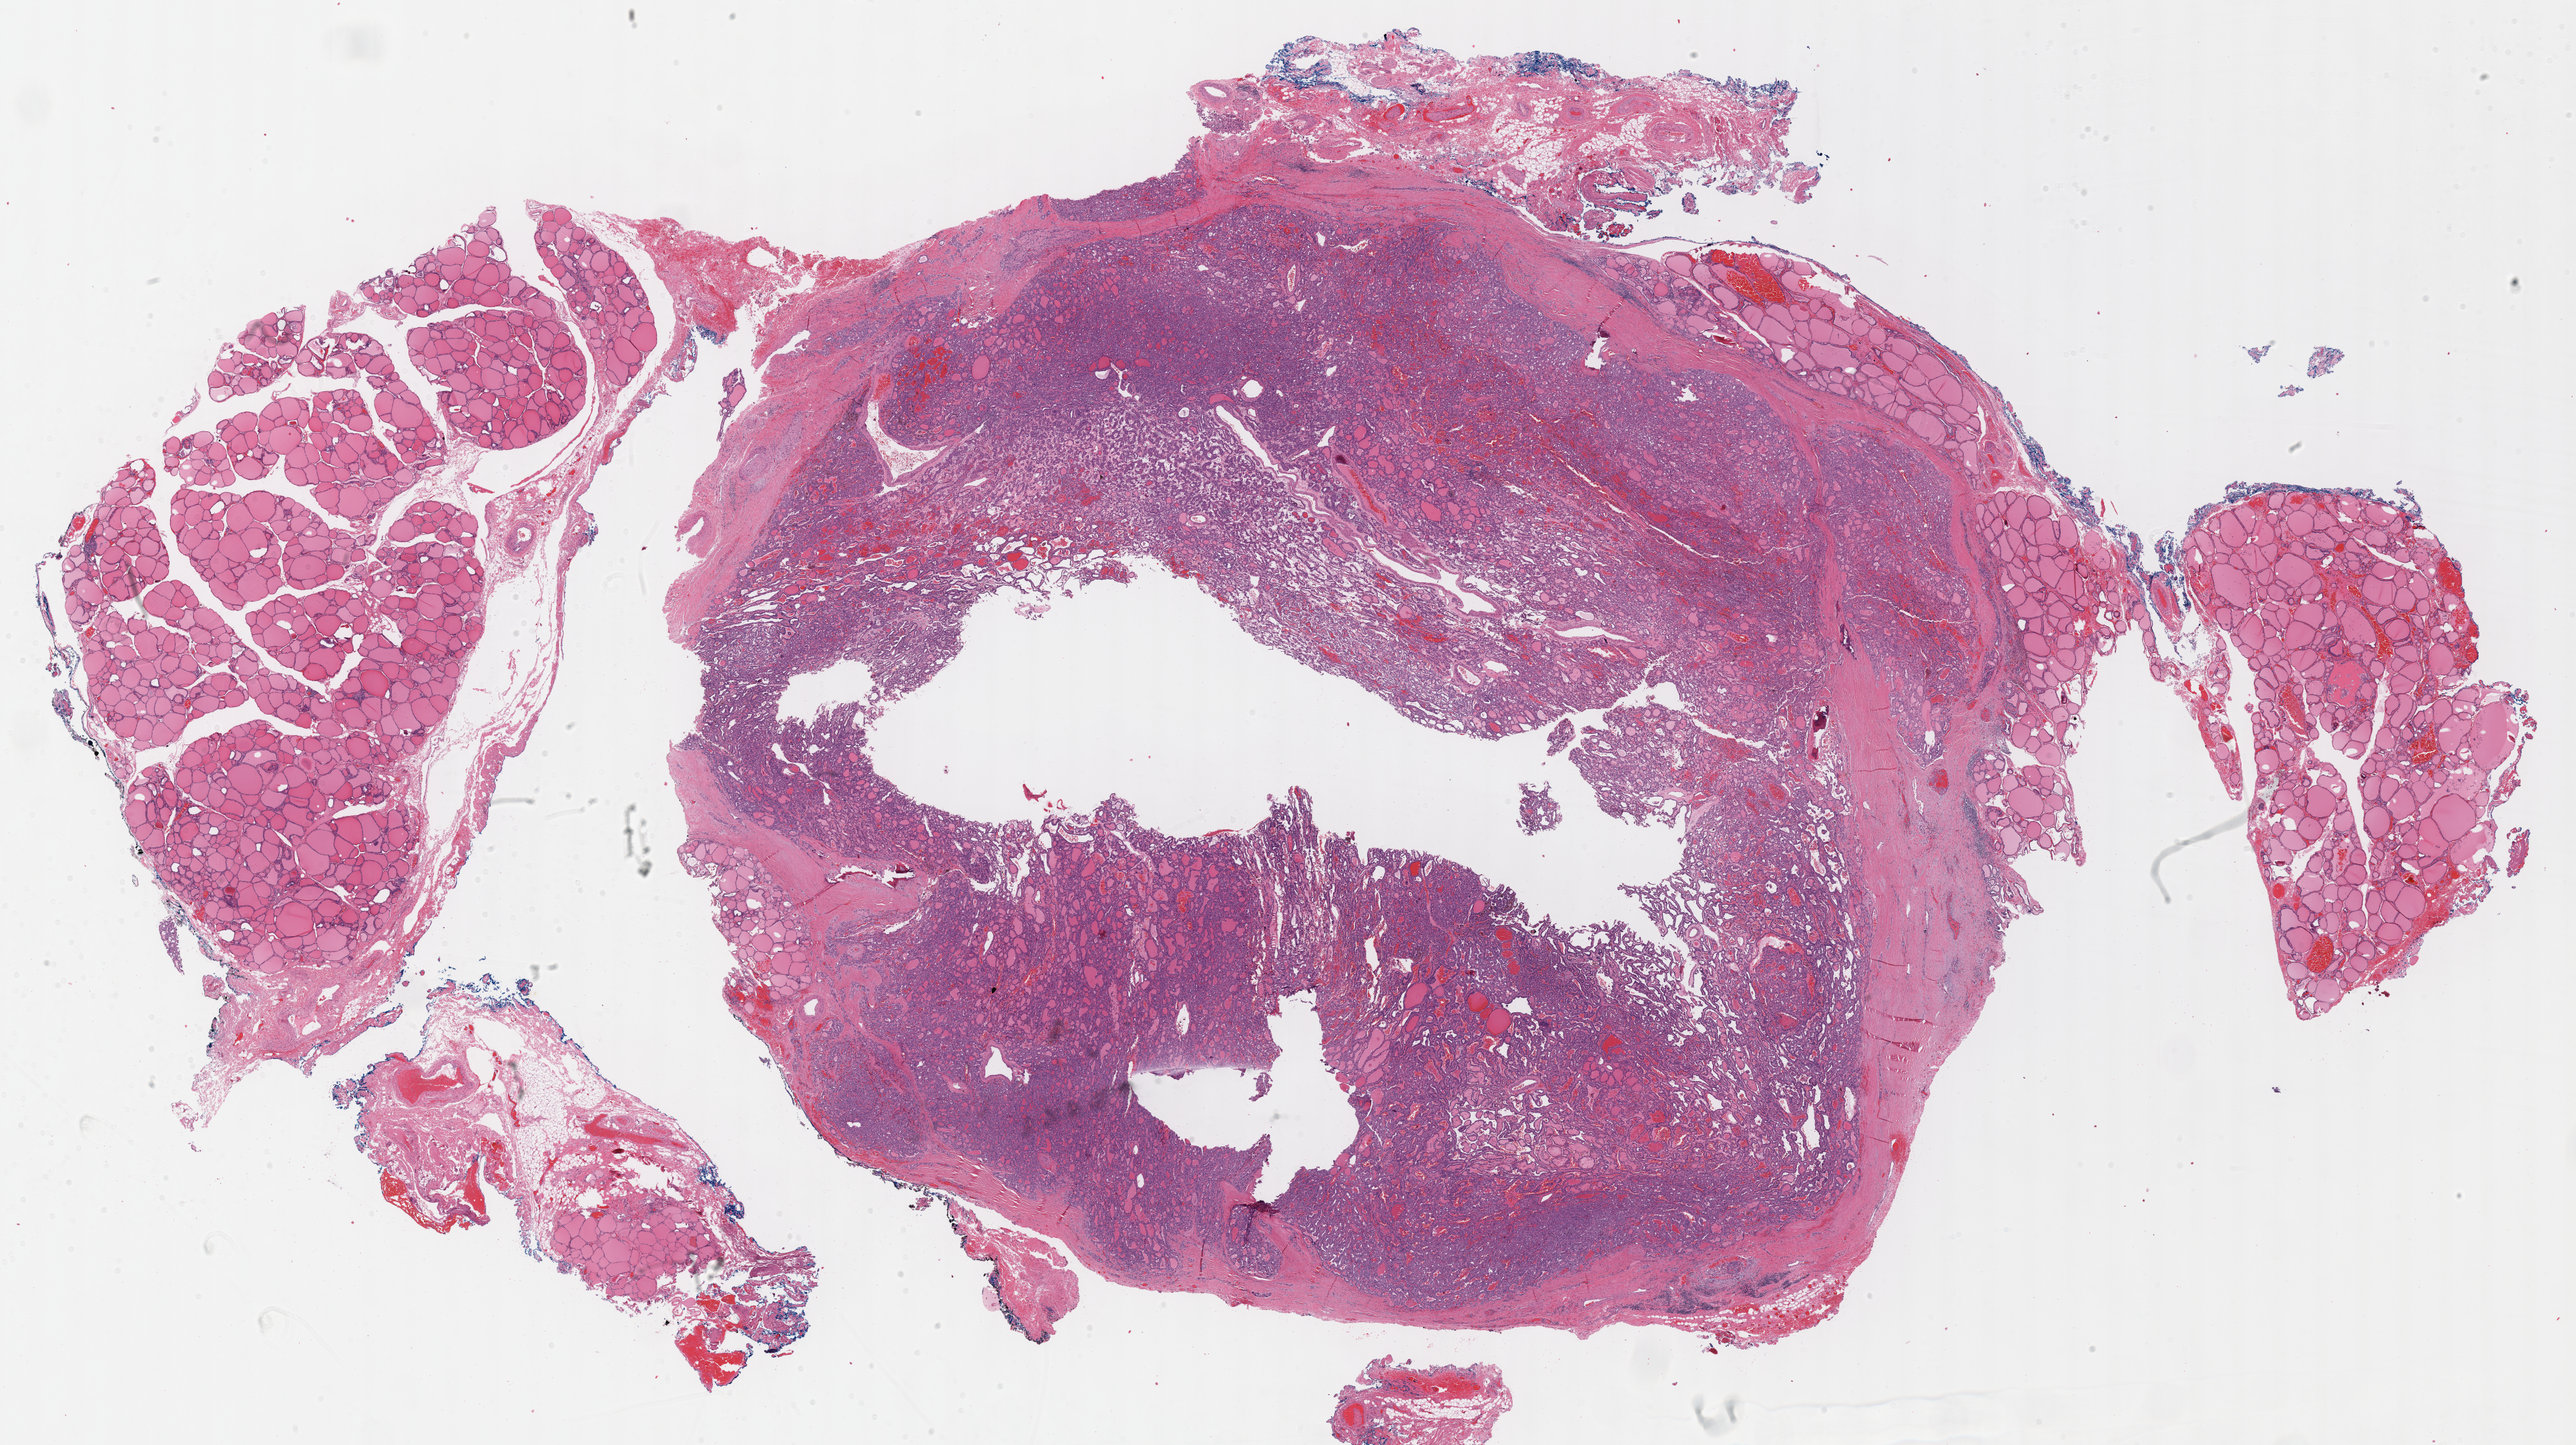
H&E-stained whole-slide image, a low-resolution overview of the entire scanned area, about 30.3 x 17.0 mm. Formalin-fixed paraffin-embedded (FFPE) diagnostic section. Primary tumour sample from the thyroid. Patient: female, age at initial diagnosis 48 years.
AJCC pathologic stage: III. TNM: T1b N1a MX. Pathologic diagnosis: Papillary adenocarcinoma, NOS (thyroid gland). Lymph nodes positive (case pathology): 2 of 4 examined.